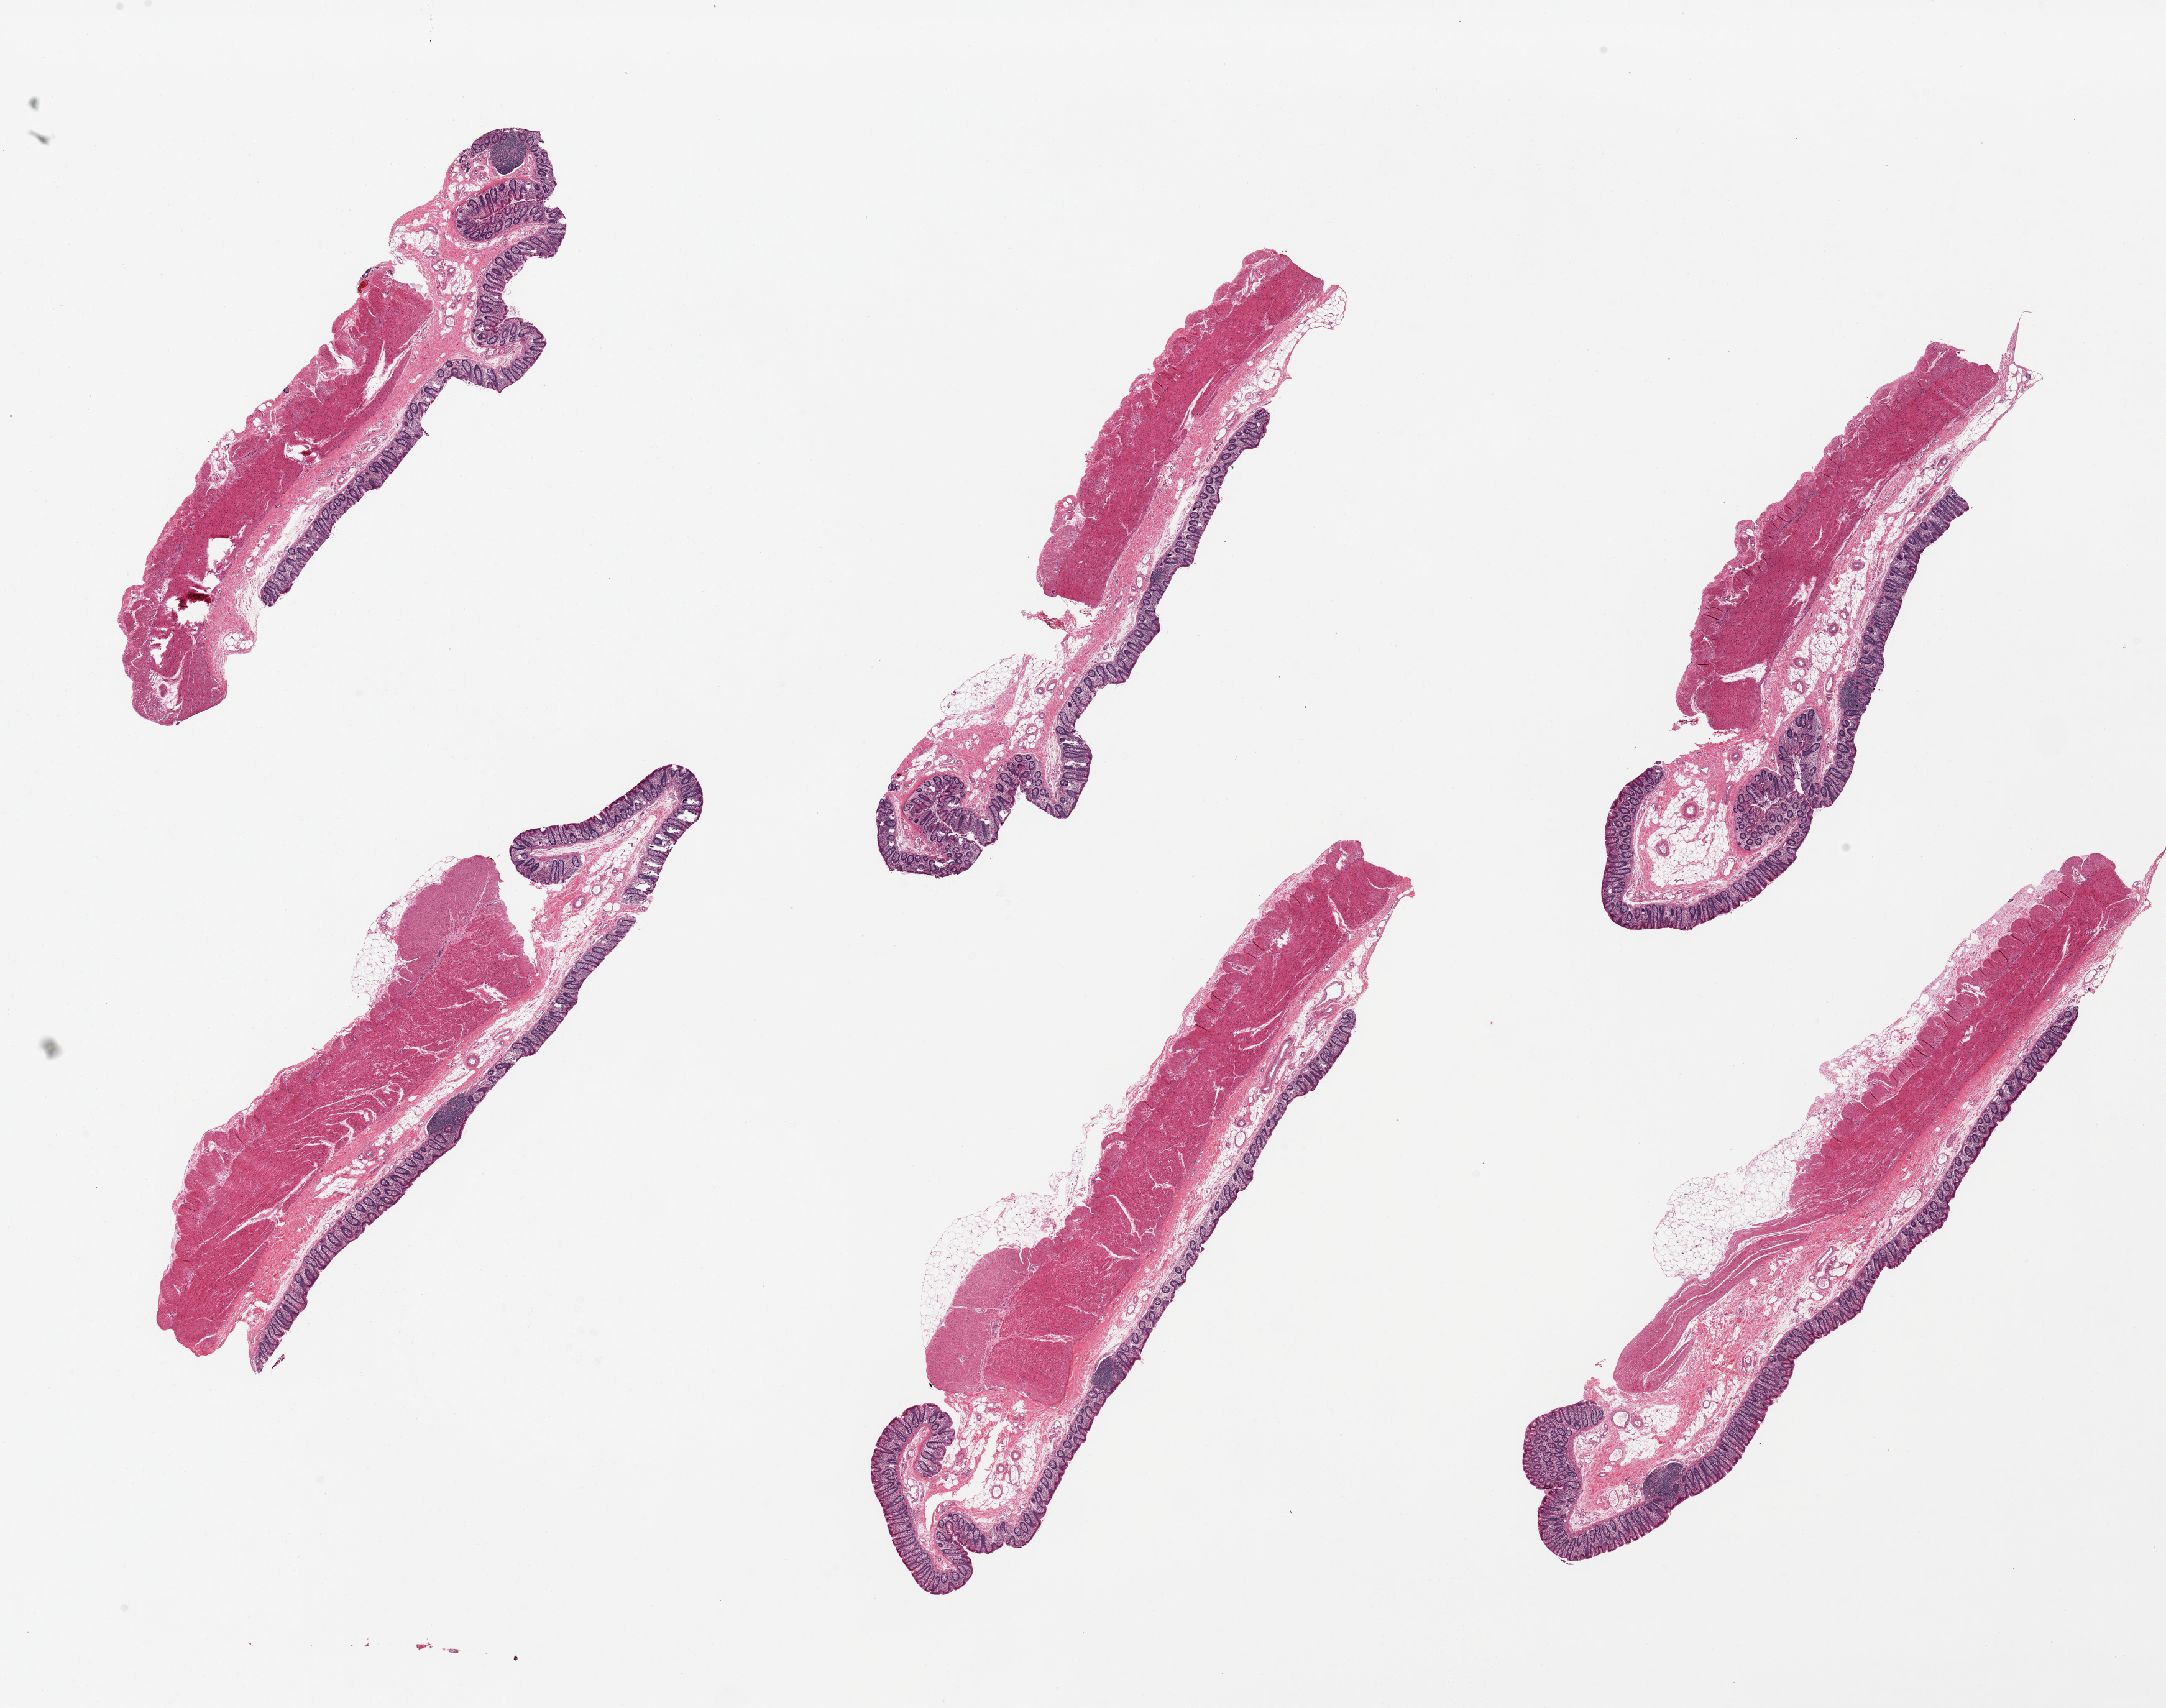
H&E whole-slide image — a low-resolution overview of the entire scanned area, about 27.6 x 21.7 mm. PAXgene-fixed paraffin-embedded (PFPE) section. Section of transverse colon (target tissue). Tissue donor sample. Male donor.
Reviewer comment on this tissue sample: 6 pieces; mucosa represents ~15% of thickness.